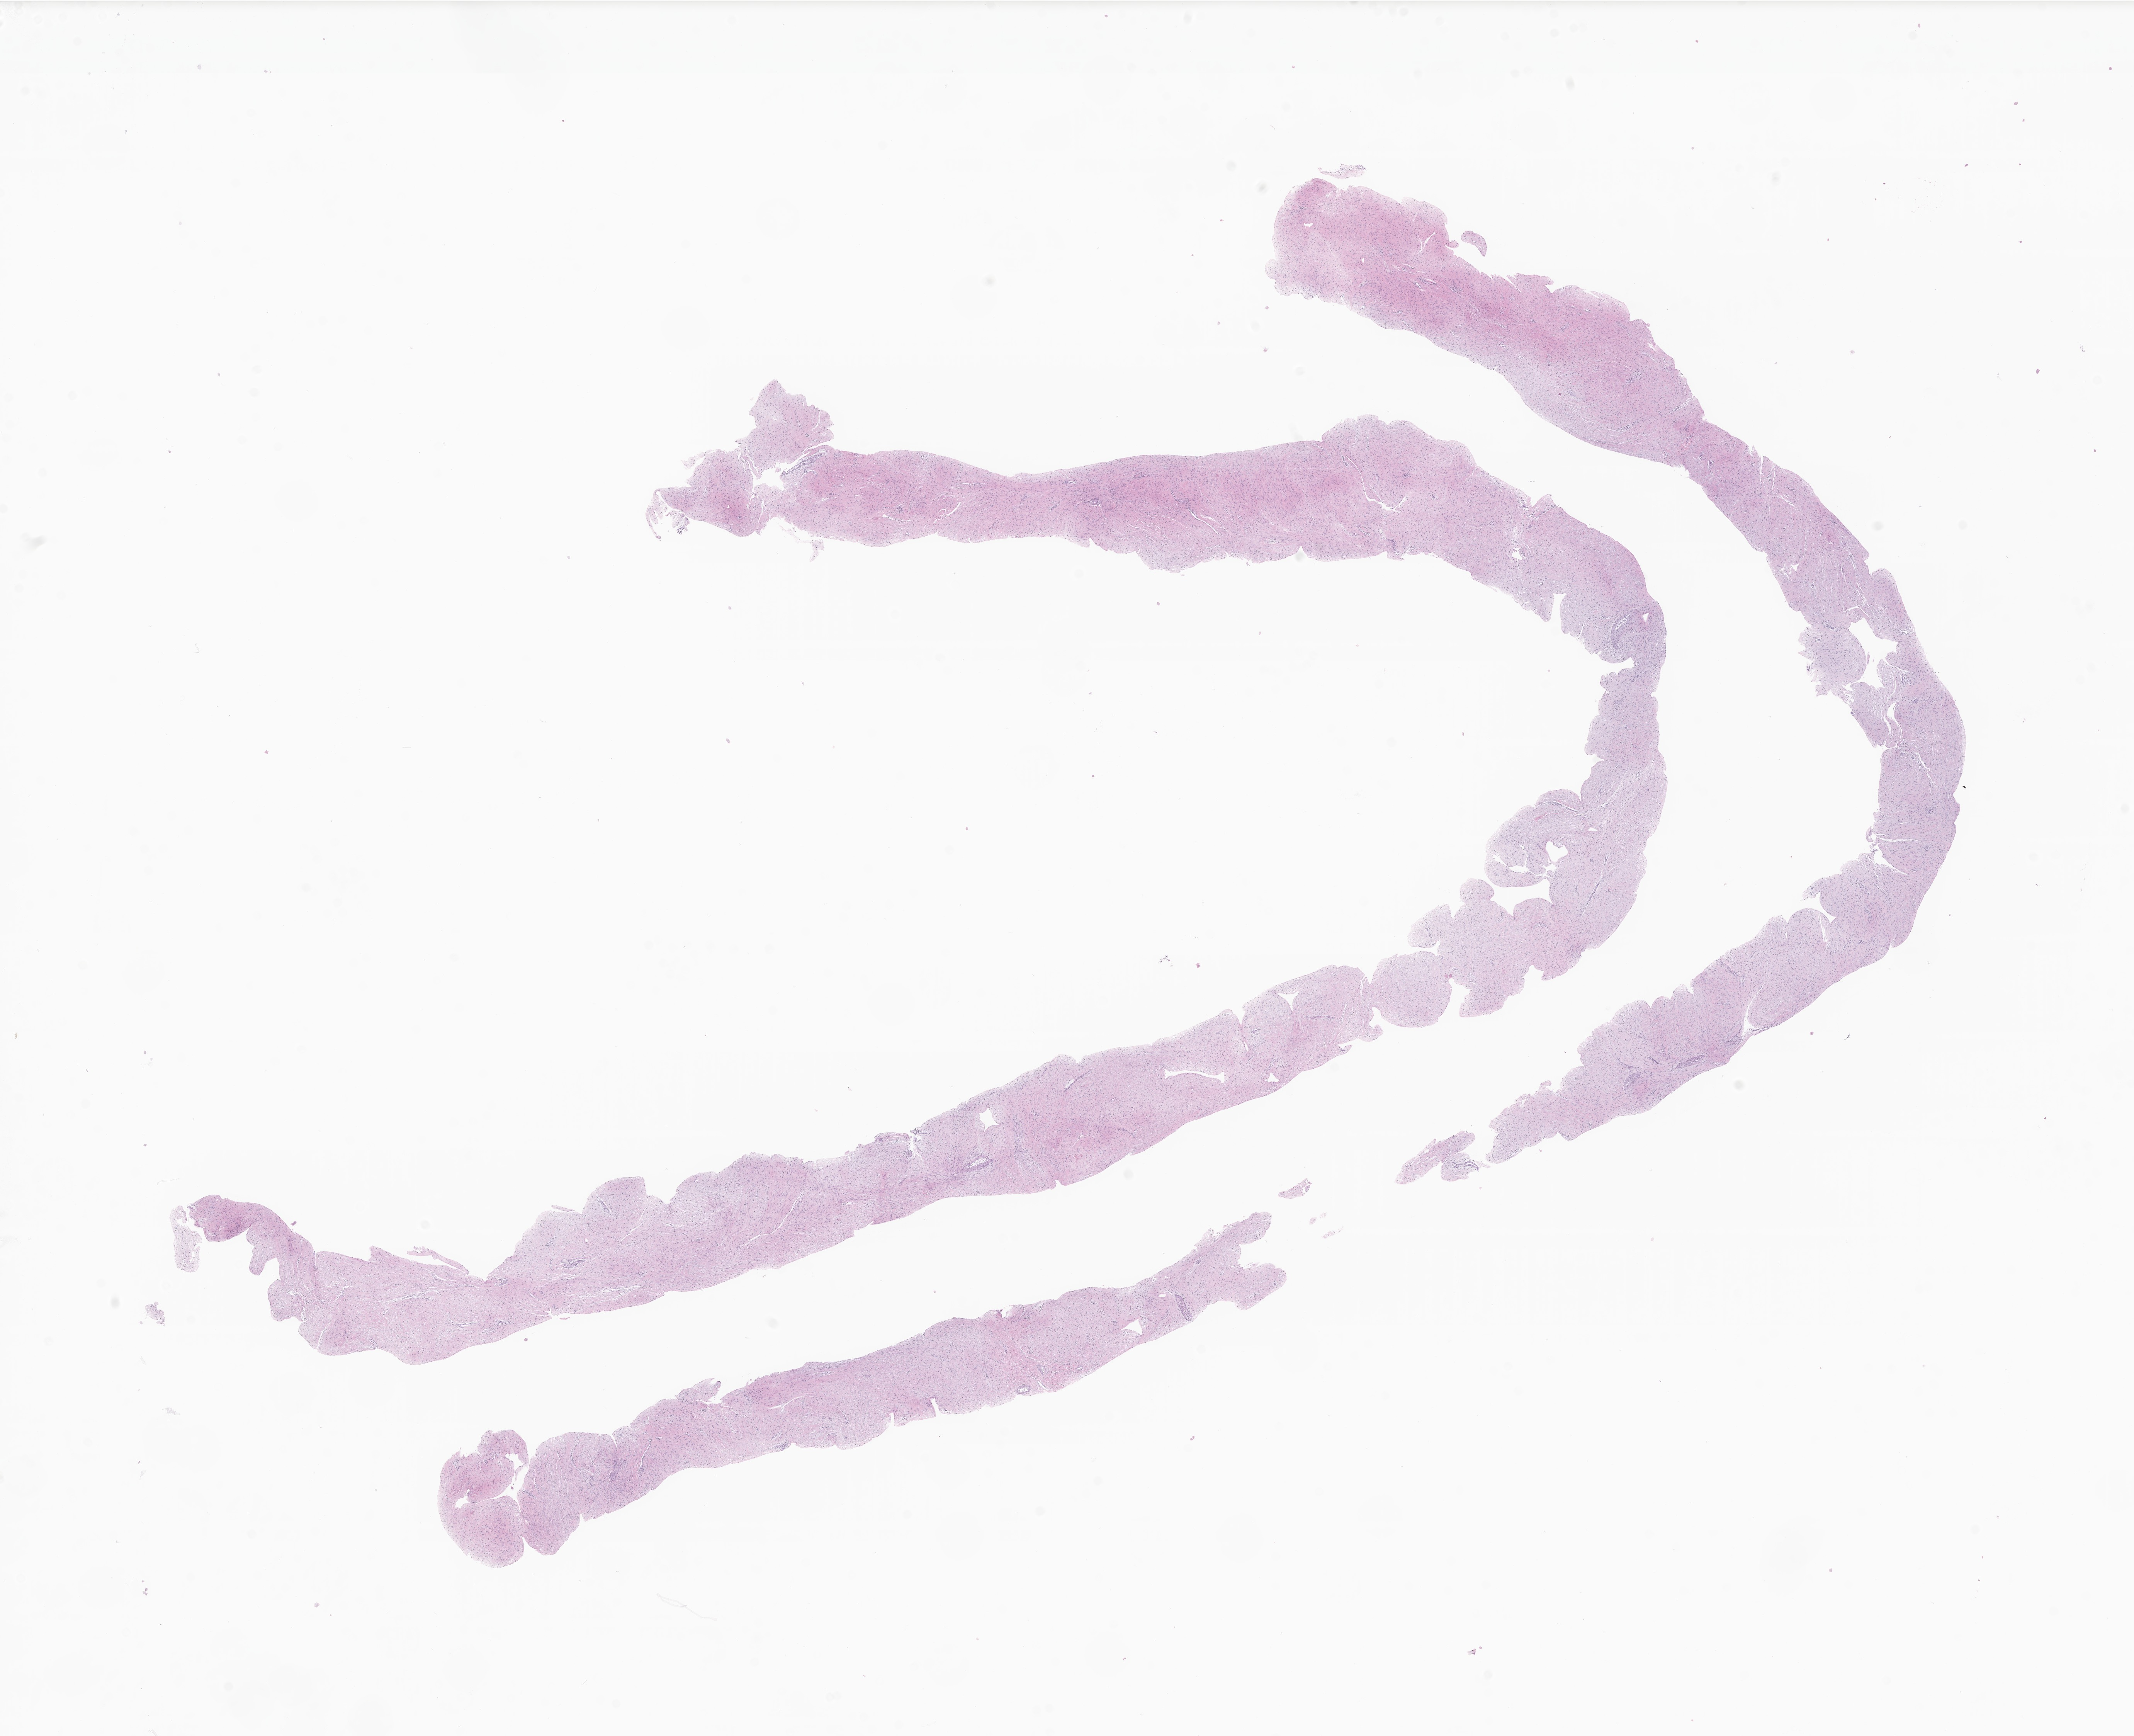
Whole-slide image, H&E stain of tumor tissue from the abdomen, a low-resolution overview of the entire scanned area, about 23.3 x 18.9 mm, formalin-fixed paraffin-embedded section. Patient female; age 209 months (17 years 5 months).
- recorded diagnosis: Abdominal fibromatosis